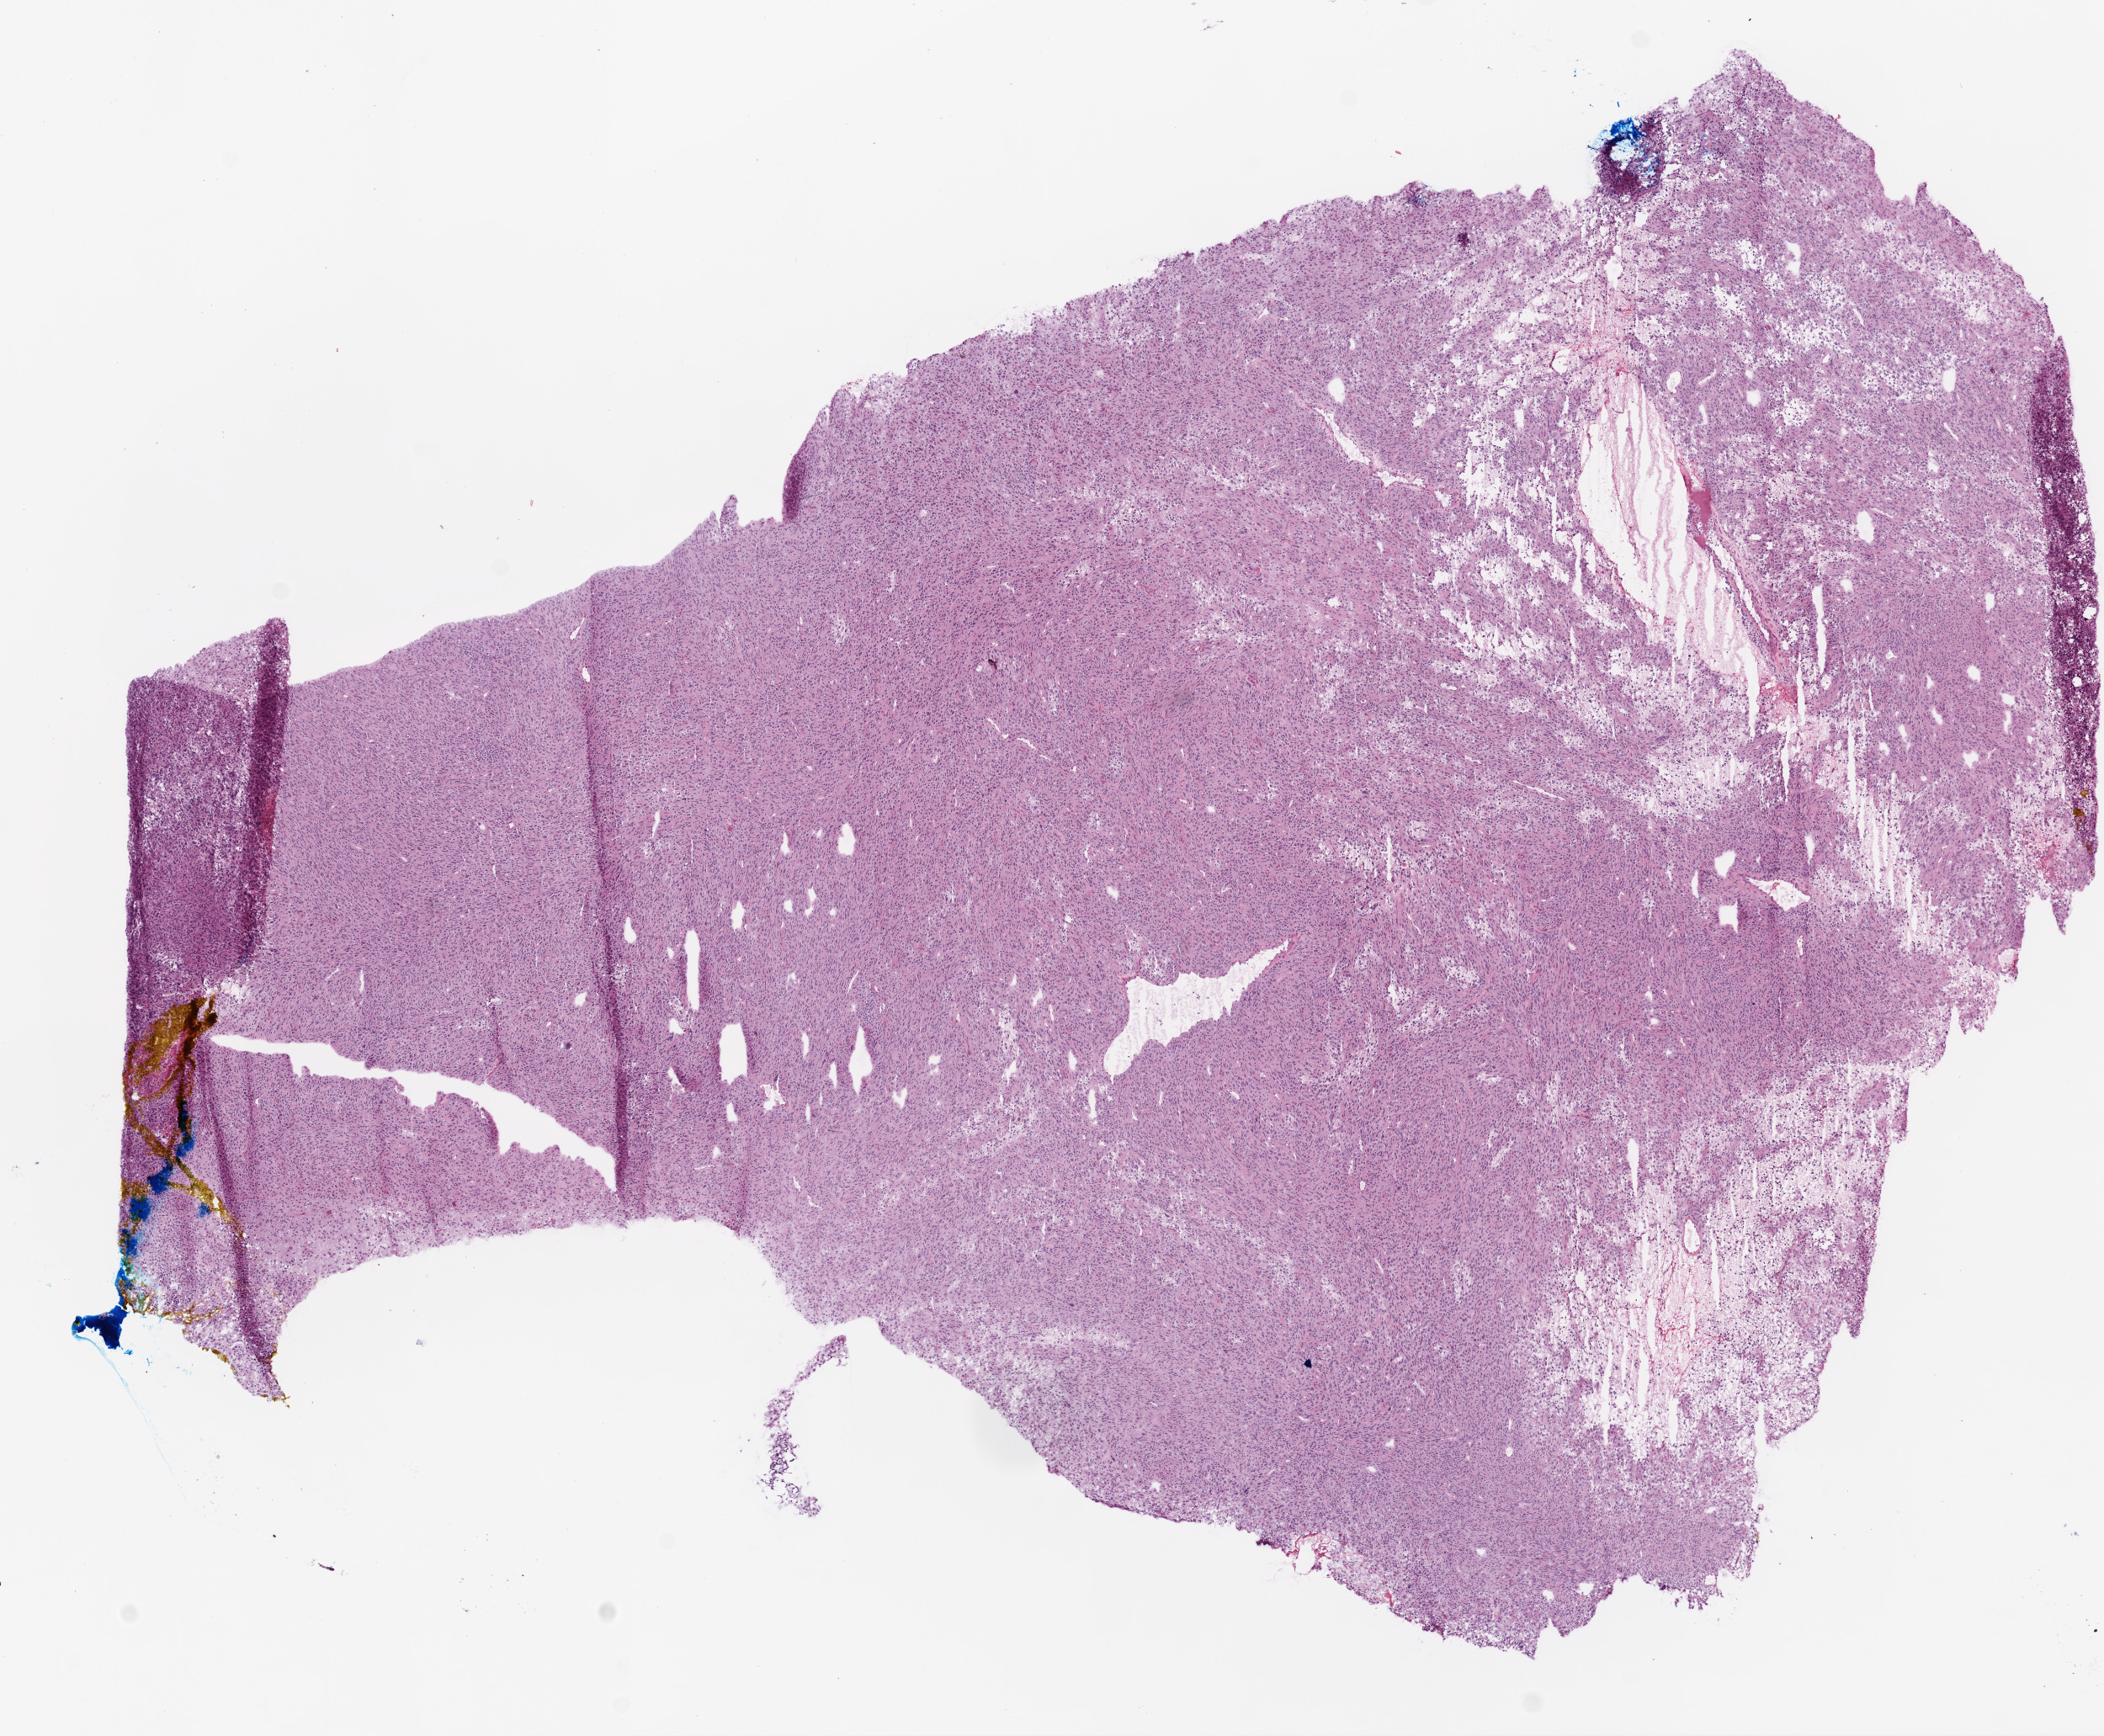
Whole-slide histology image, Hematoxylin and eosin (H&E) stained, low-resolution overview of the scanned area, about 10.0 x 8.3 mm; frozen section; primary tumour sample from the brain. Patient: female, age at initial diagnosis 49 years. Slide review estimates, as recorded: tumour cells 95%, tumour nuclei 95%, normal cells 0%, stromal cells 0%, necrosis 5%.
- diagnosis: Glioblastoma